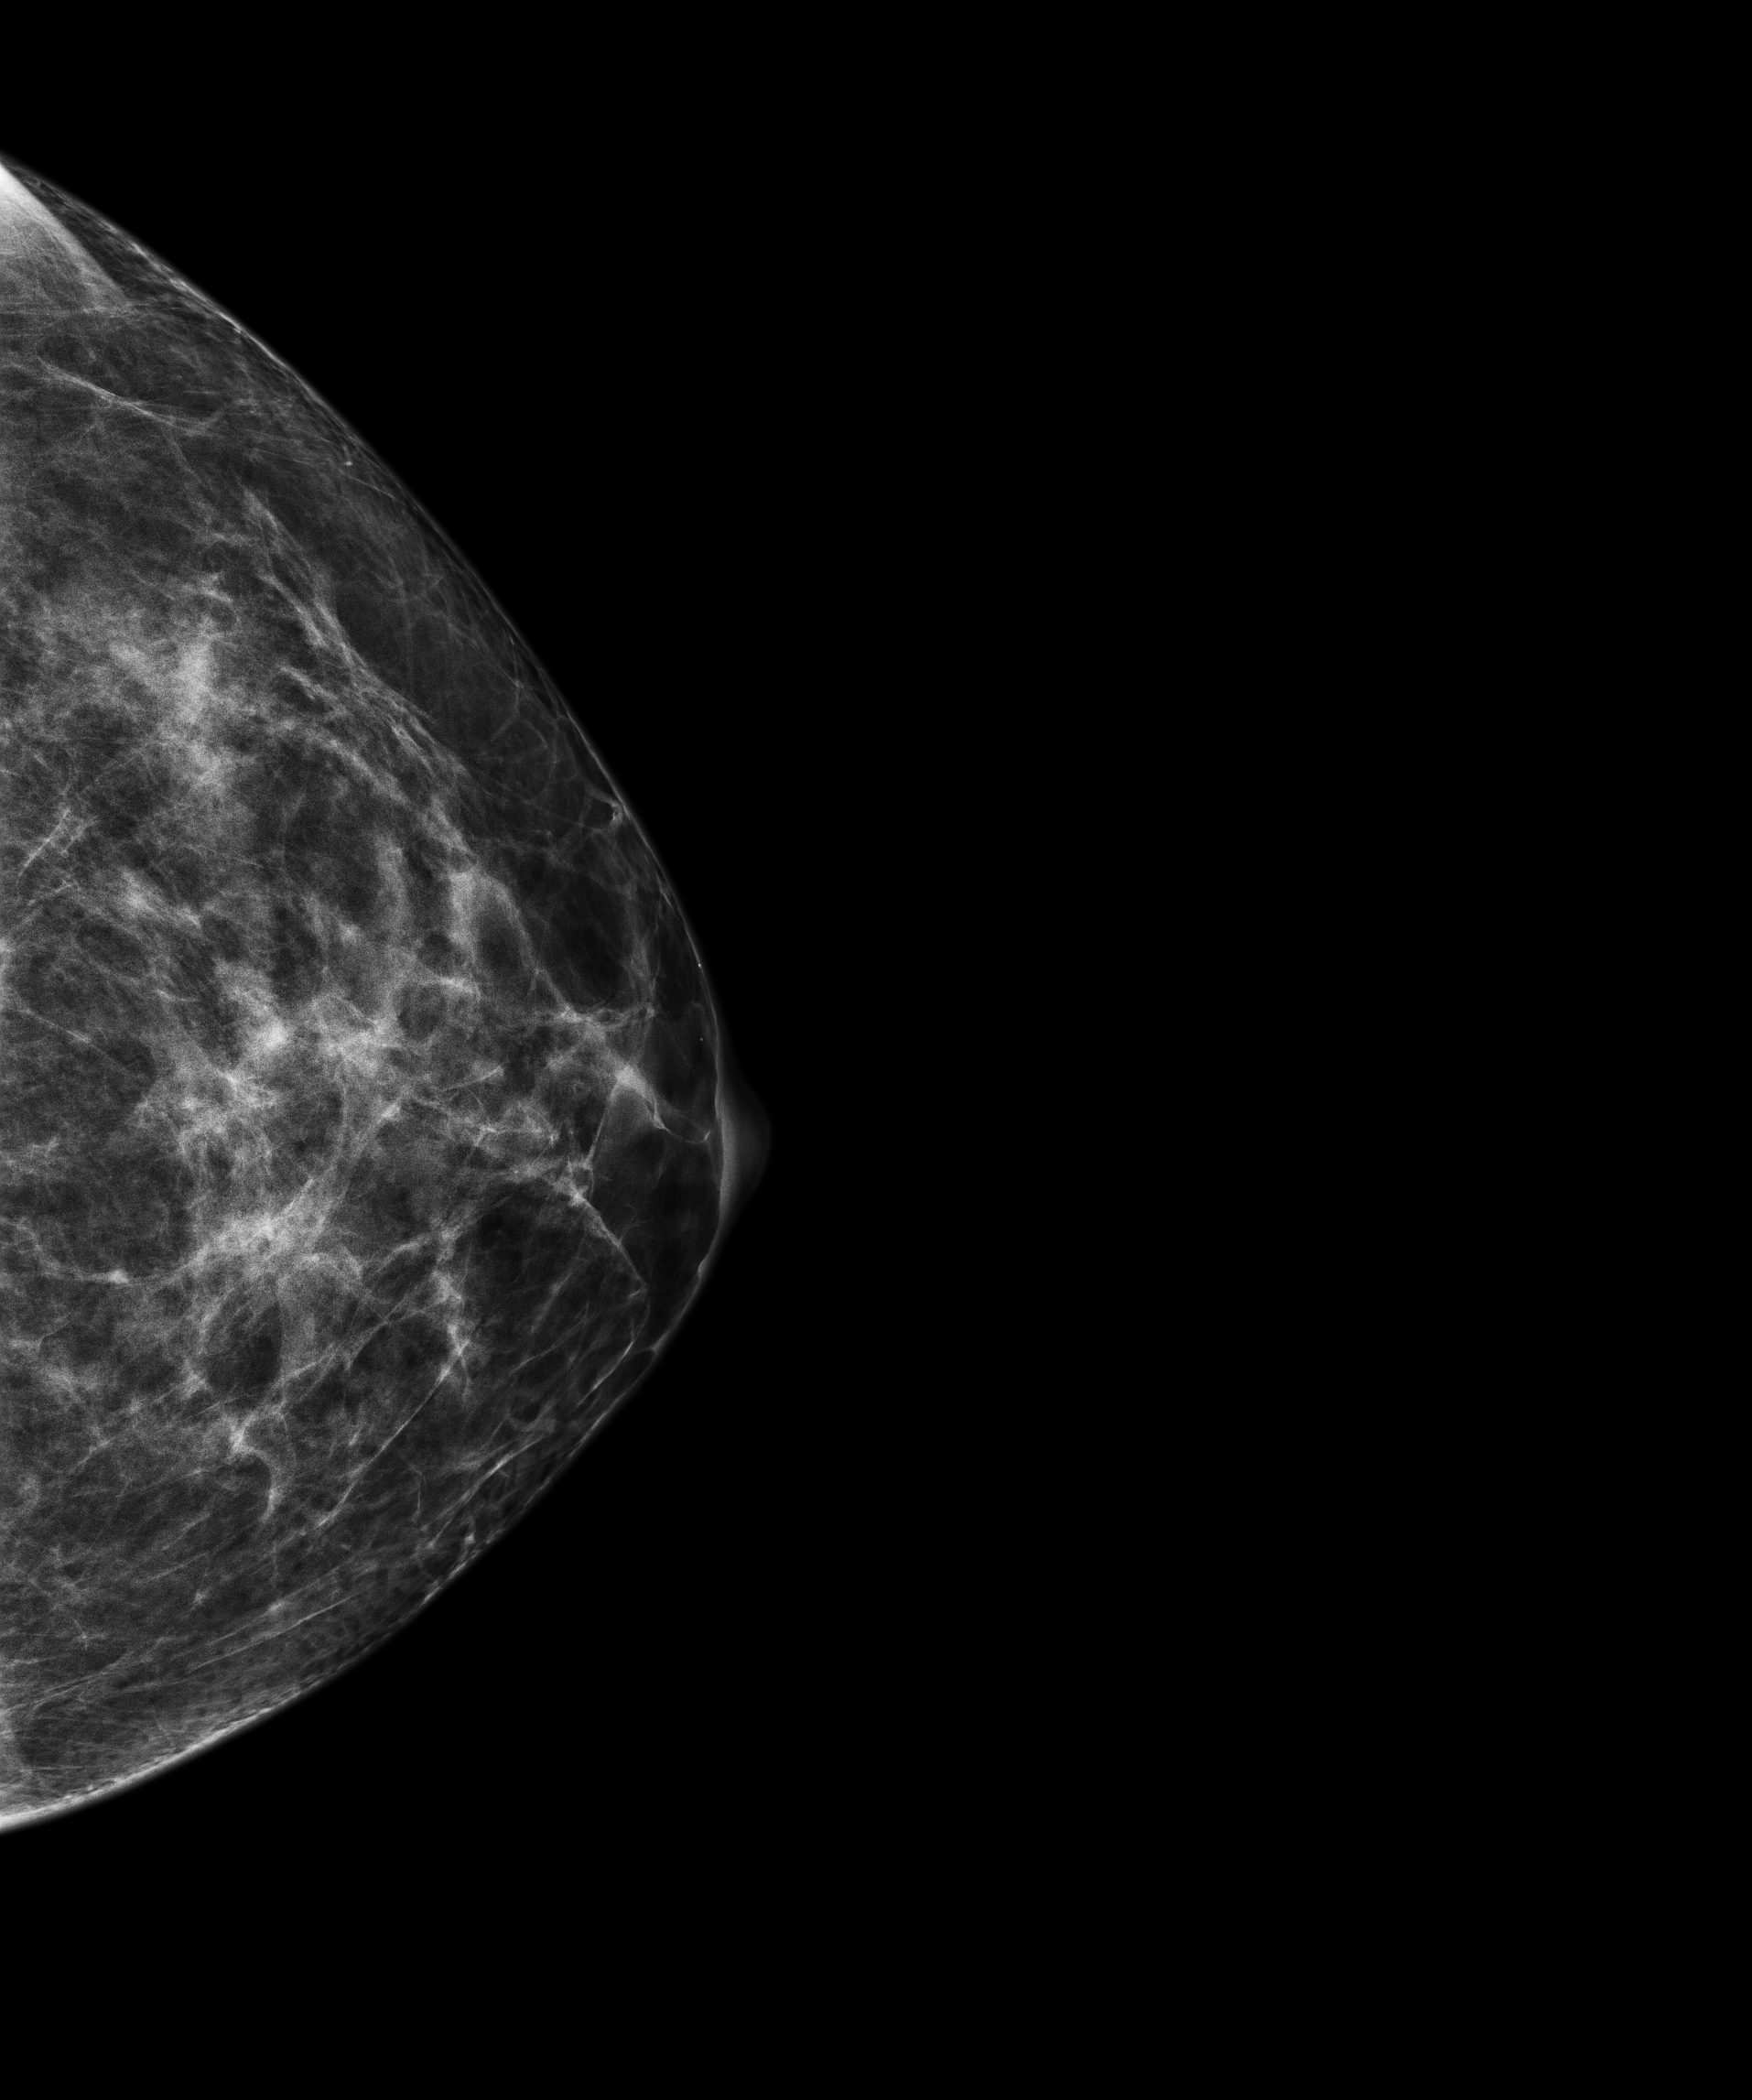
Full-field digital mammogram (FFDM); left breast; cranio-caudal projection; screening examination; compressed breast thickness 60.3 mm. Patient: female, 43 years.
- breast density at the screening exam (both breasts): scattered fibroglandular densities (BI-RADS density category b)
- final BI-RADS assessment for this screening round (tomosynthesis exam, both breasts): category 1
- recall: no recall after this screen